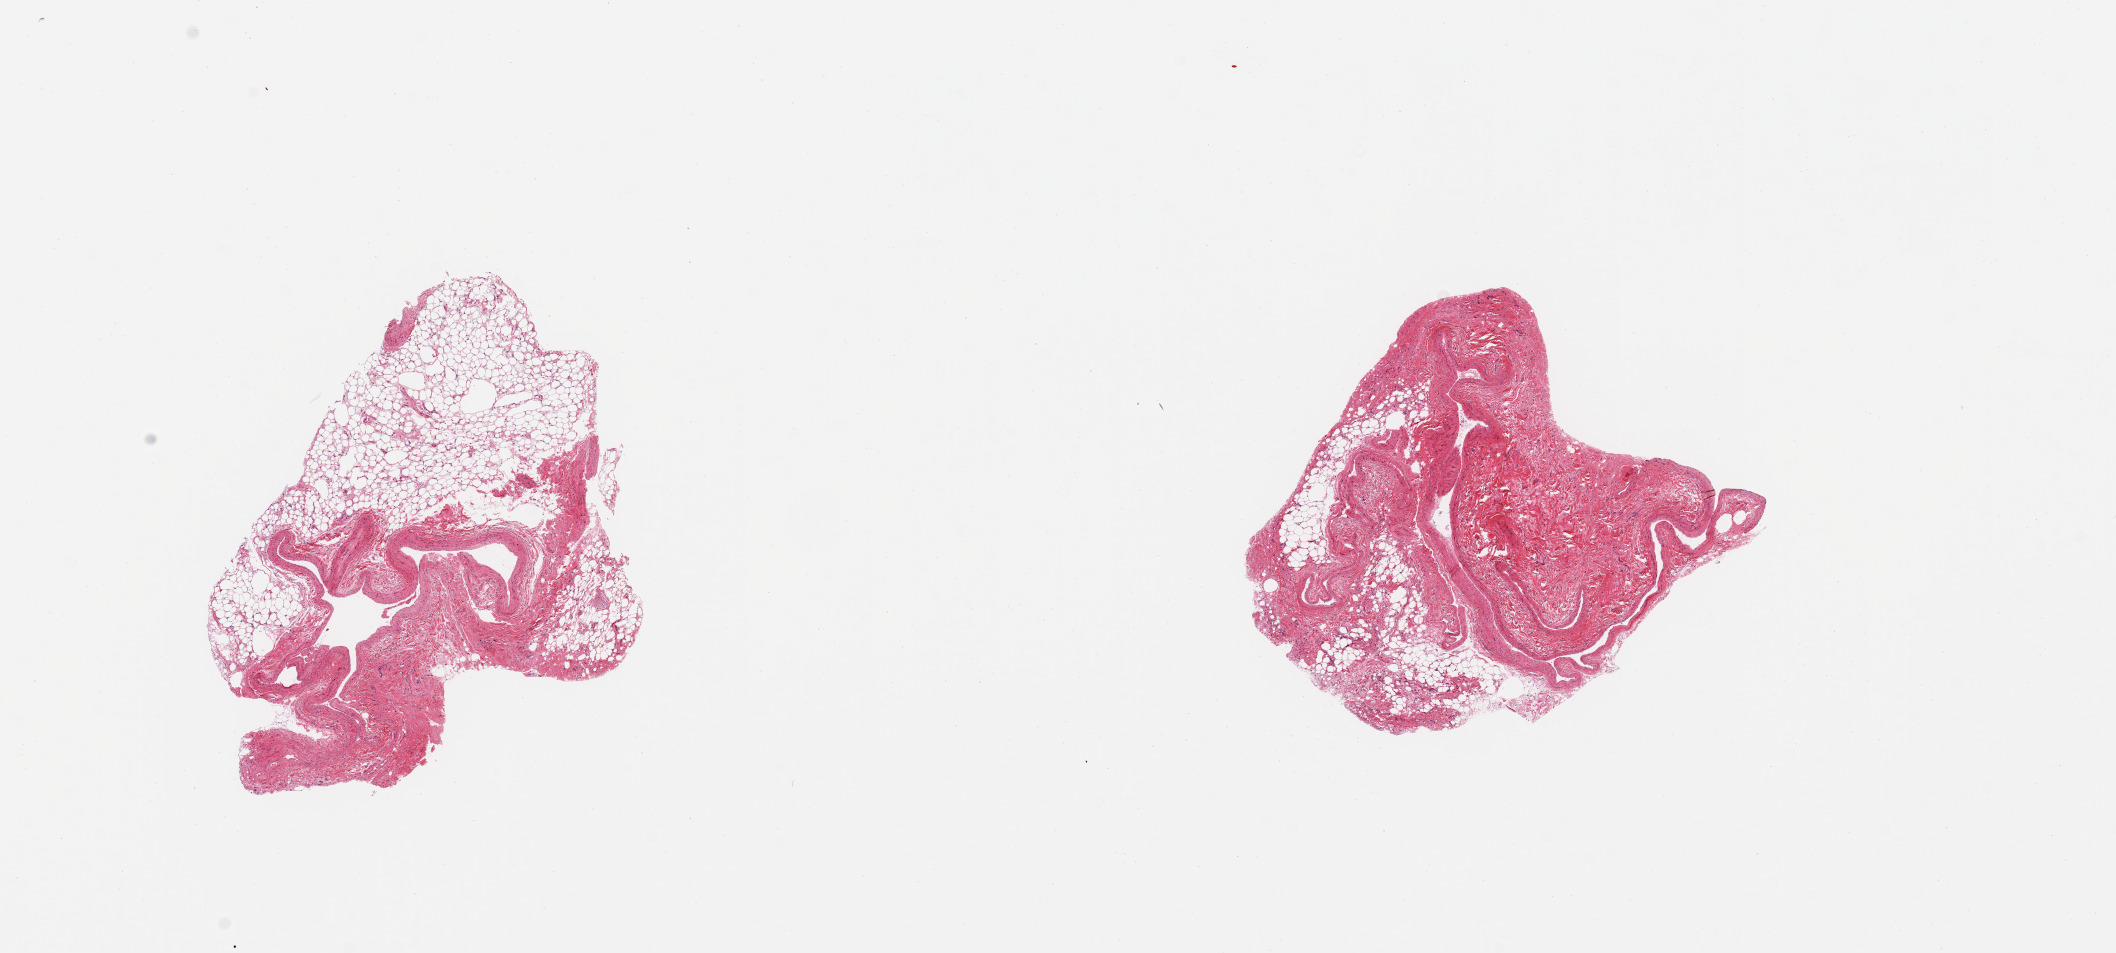
H&E whole-slide image, low-resolution overview of the scanned area, about 16.7 x 7.5 mm; PAXgene-fixed, paraffin-embedded tissue; sampled site (target tissue): coronary artery; tissue donor sample. Male donor.
Review note (as recorded): 2 pieces, not artery but venous, and ~60-70% of specimen is non-target fat/fibrous tissue.